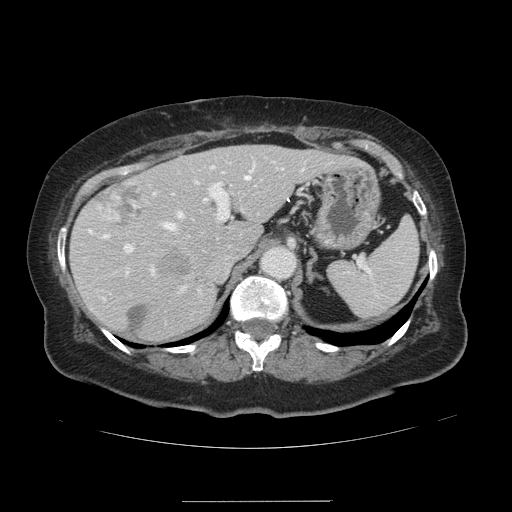
Contrast-enhanced abdominal CT, one axial slice; soft-tissue window (W 400 / L 40 HU); 512 × 512 image matrix, field of view 393 × 393 mm. Female patient, age 74 years. From the clinical record (not read from this slice): diagnosis: colorectal cancer liver metastases, imaged before liver resection.
Structures marked on this image (expert manual segmentation):
- hepatic veins: bounding box <103,176,249,293> (left, top, right, bottom; pixels)
- liver: <72,146,346,340>
- planned liver remnant (the part of the liver to remain after resection): <72,146,346,340>
- portal vein (with intrahepatic branches): <124,164,303,272>
- liver metastasis: <97,180,145,231>
- liver metastasis: <129,304,148,331>
- liver metastasis: <161,255,191,275>